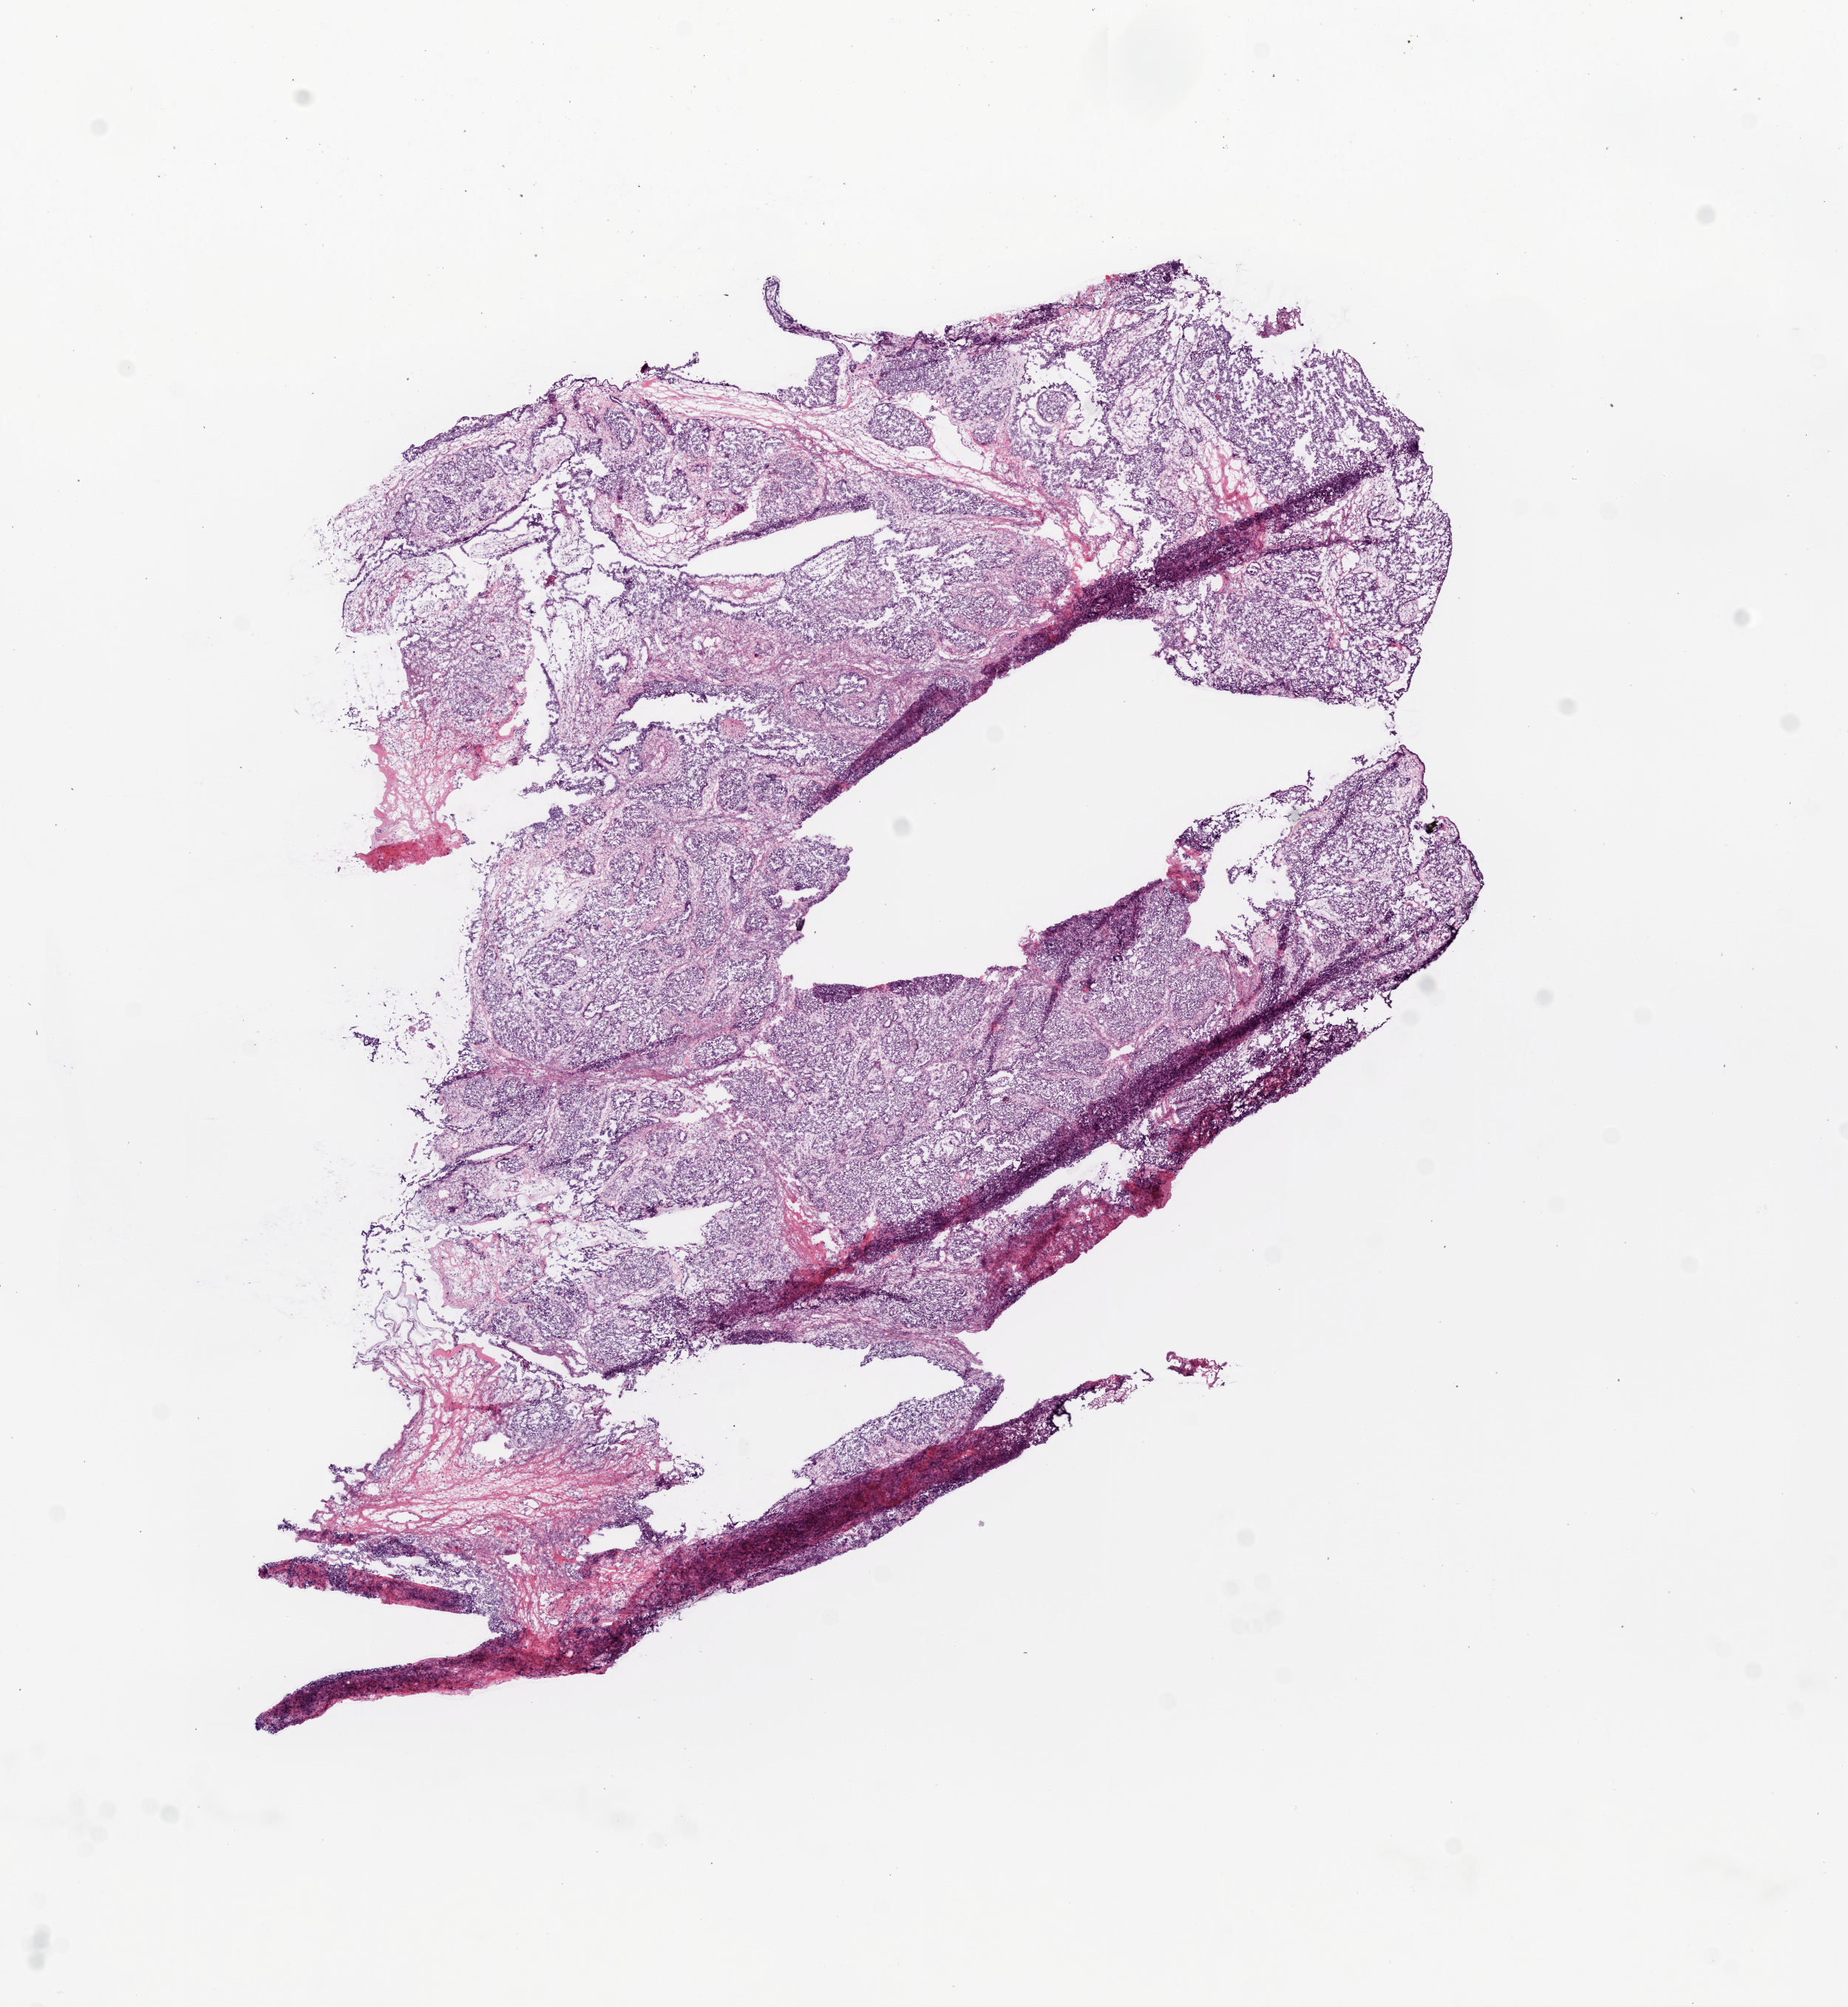
H&E-stained whole-slide image, shown as a low-resolution overview of the whole scanned area (about 10.0 x 10.9 mm, slide scanned at 20x). Frozen section. Ovary, primary tumour sample. Female patient; age at initial diagnosis 66 years. Histologic grade: G3 (poorly differentiated). Composition of this section per pathologist review: tumour cells 90%, tumour nuclei 90%, normal cells 0%, stromal cells 10%, necrosis 0%.
• FIGO stage: IIIC
• pathologic diagnosis: Serous cystadenocarcinoma, NOS
• laterality: bilateral